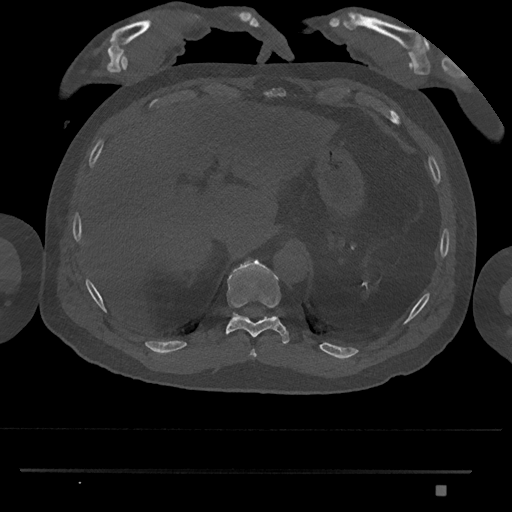
CT including the spine, one axial slice. Slice 996 of 1134 in the series (ordered by position). Bone window (W 1800 / L 400 HU). 512 × 512 image matrix, field of view 429 × 429 mm. Male patient, age 65 years. From the clinical record (not read from this slice): primary cancer: prostate.
Structures marked on this image (semi-automatic segmentation, software-assisted and operator-edited):
- T10 vertebra: bounding box (x1, y1, x2, y2) in pixels: (226, 259, 289, 345)
- T11 vertebra: (233, 312, 245, 318)
- T9 vertebra: (249, 349, 257, 359)